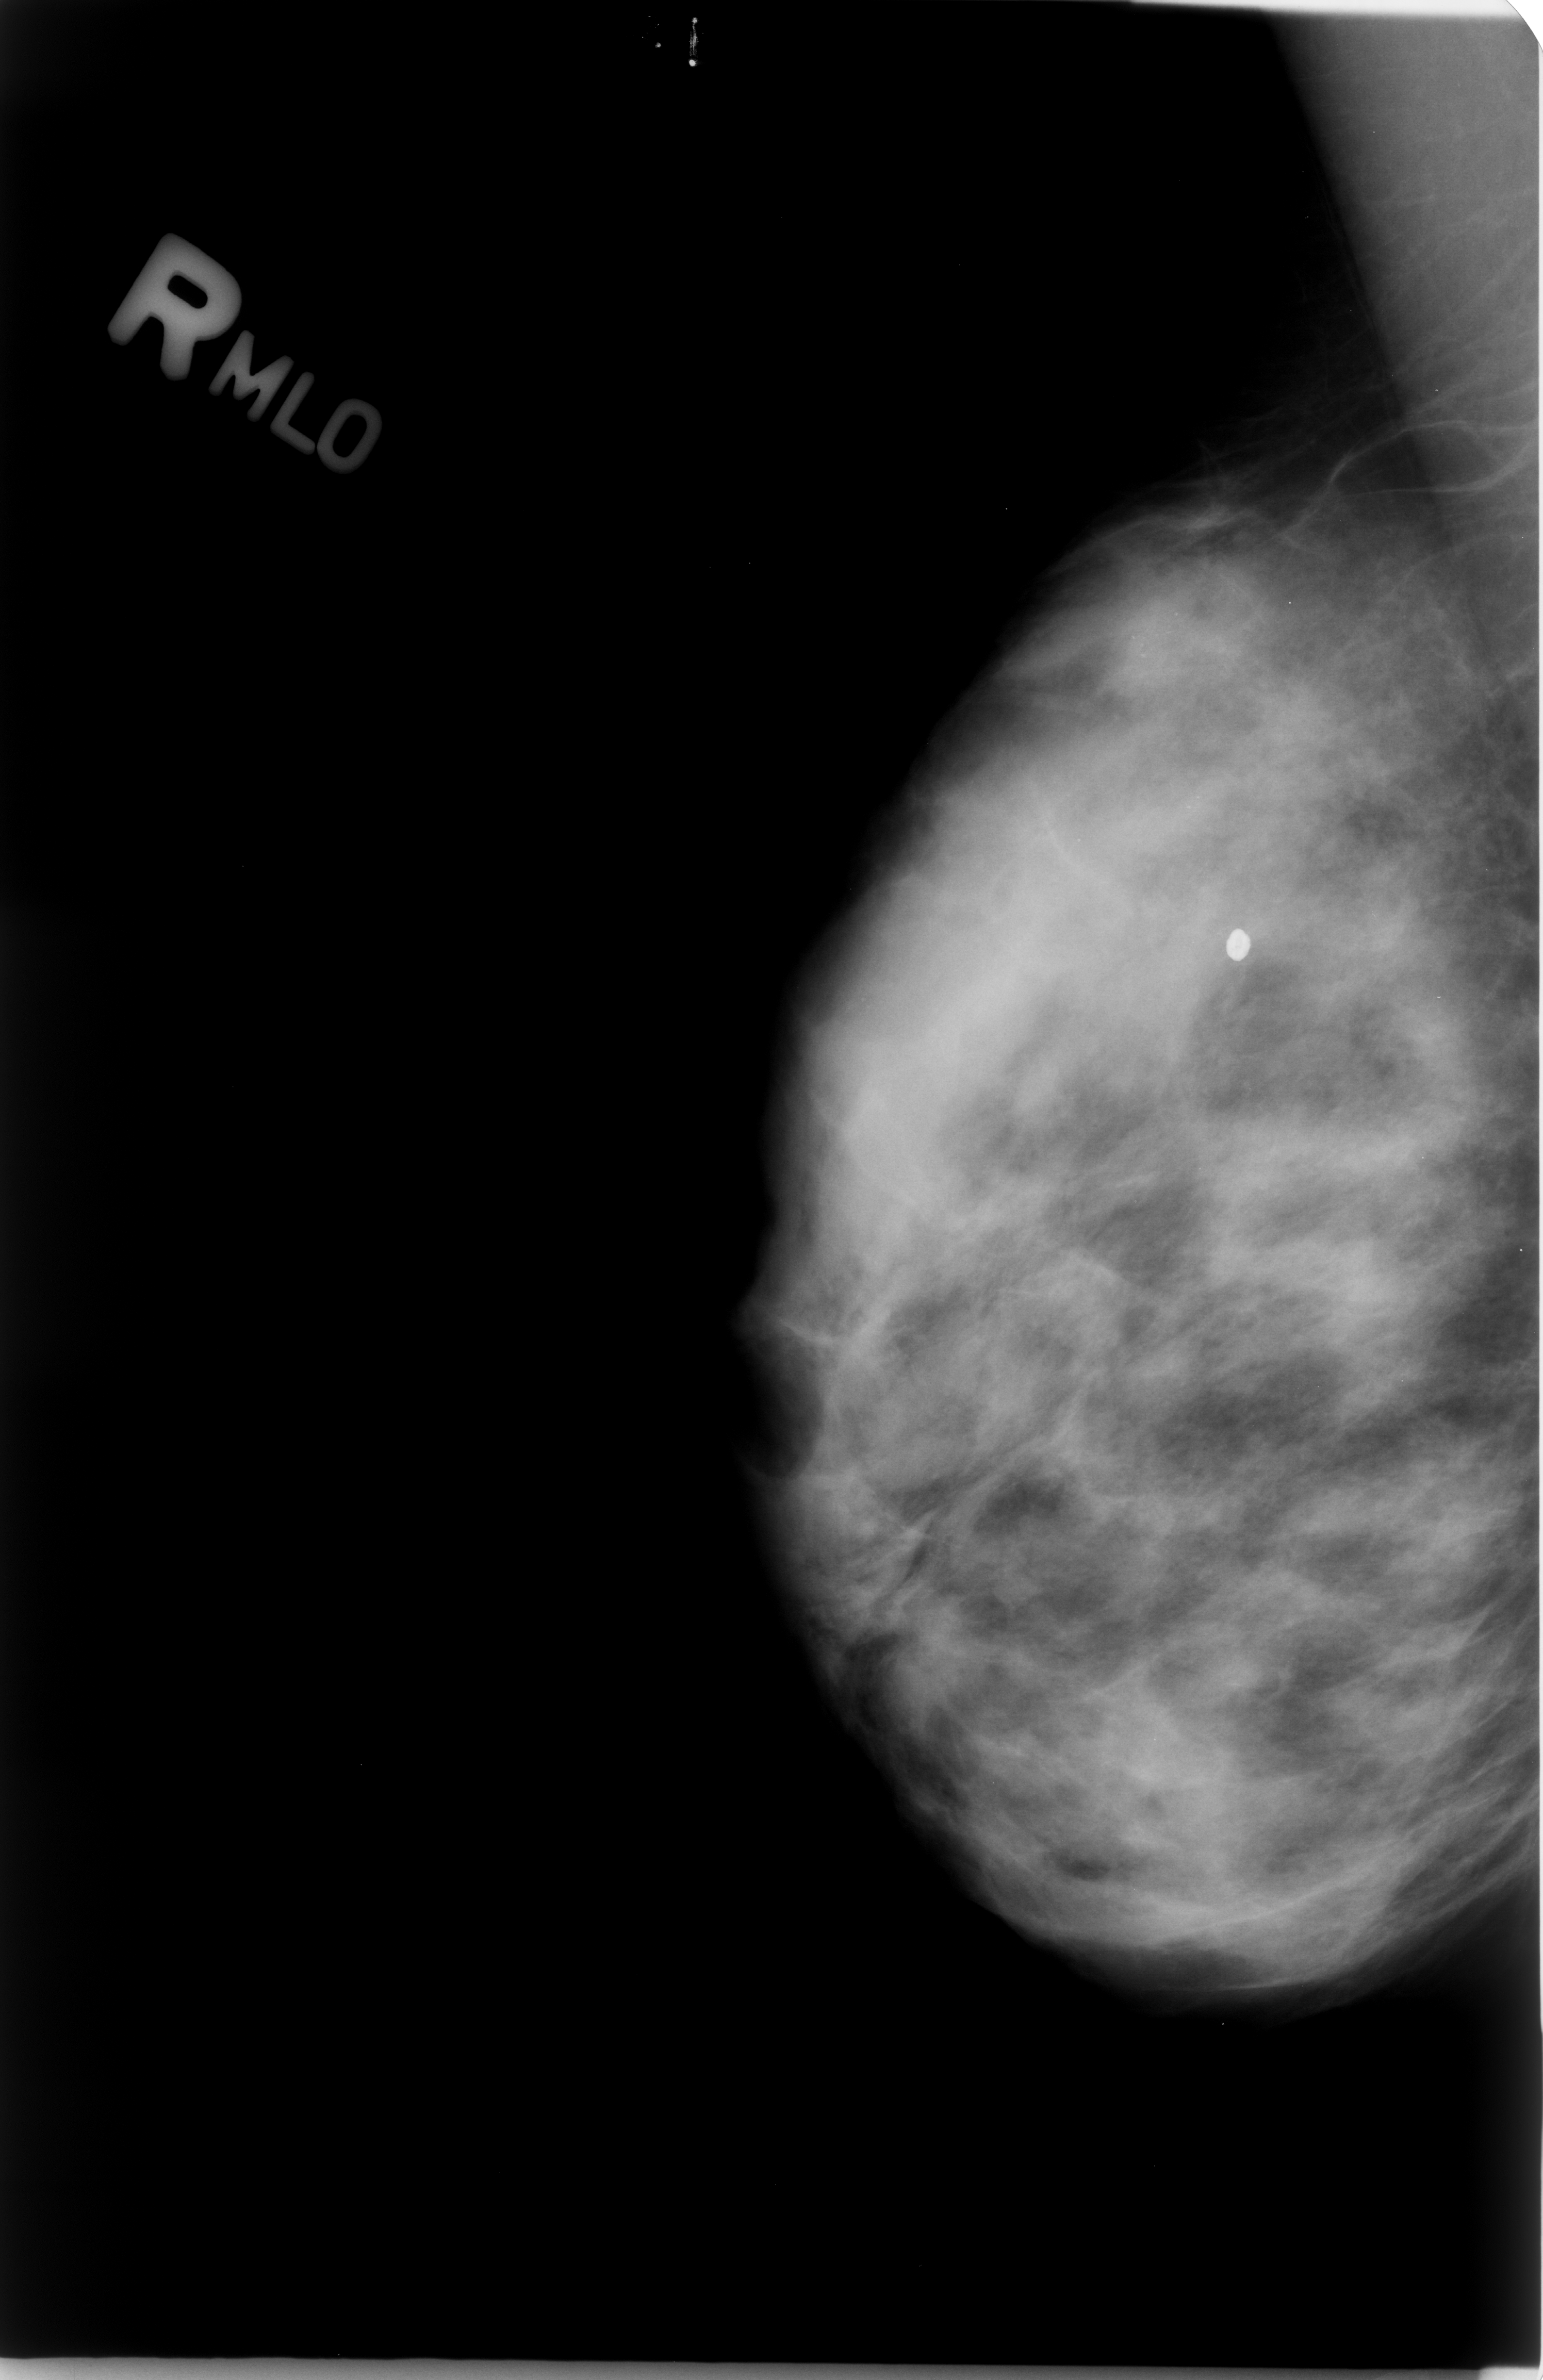
Scanned film-screen mammogram; right breast; MLO view; BI-RADS breast density category 3 (scale 1–4); 1543 × 2380 image matrix.
Expert-marked regions of interest on this film, with their recorded descriptors:
- calcifications, morphology punctate, distribution clustered; BI-RADS assessment category 4; subtlety rating 3 on a 1 (subtle) to 5 (obvious) scale; pathology (as recorded): benign: bounding box <1122,763,1243,871> (left, top, right, bottom; pixels)